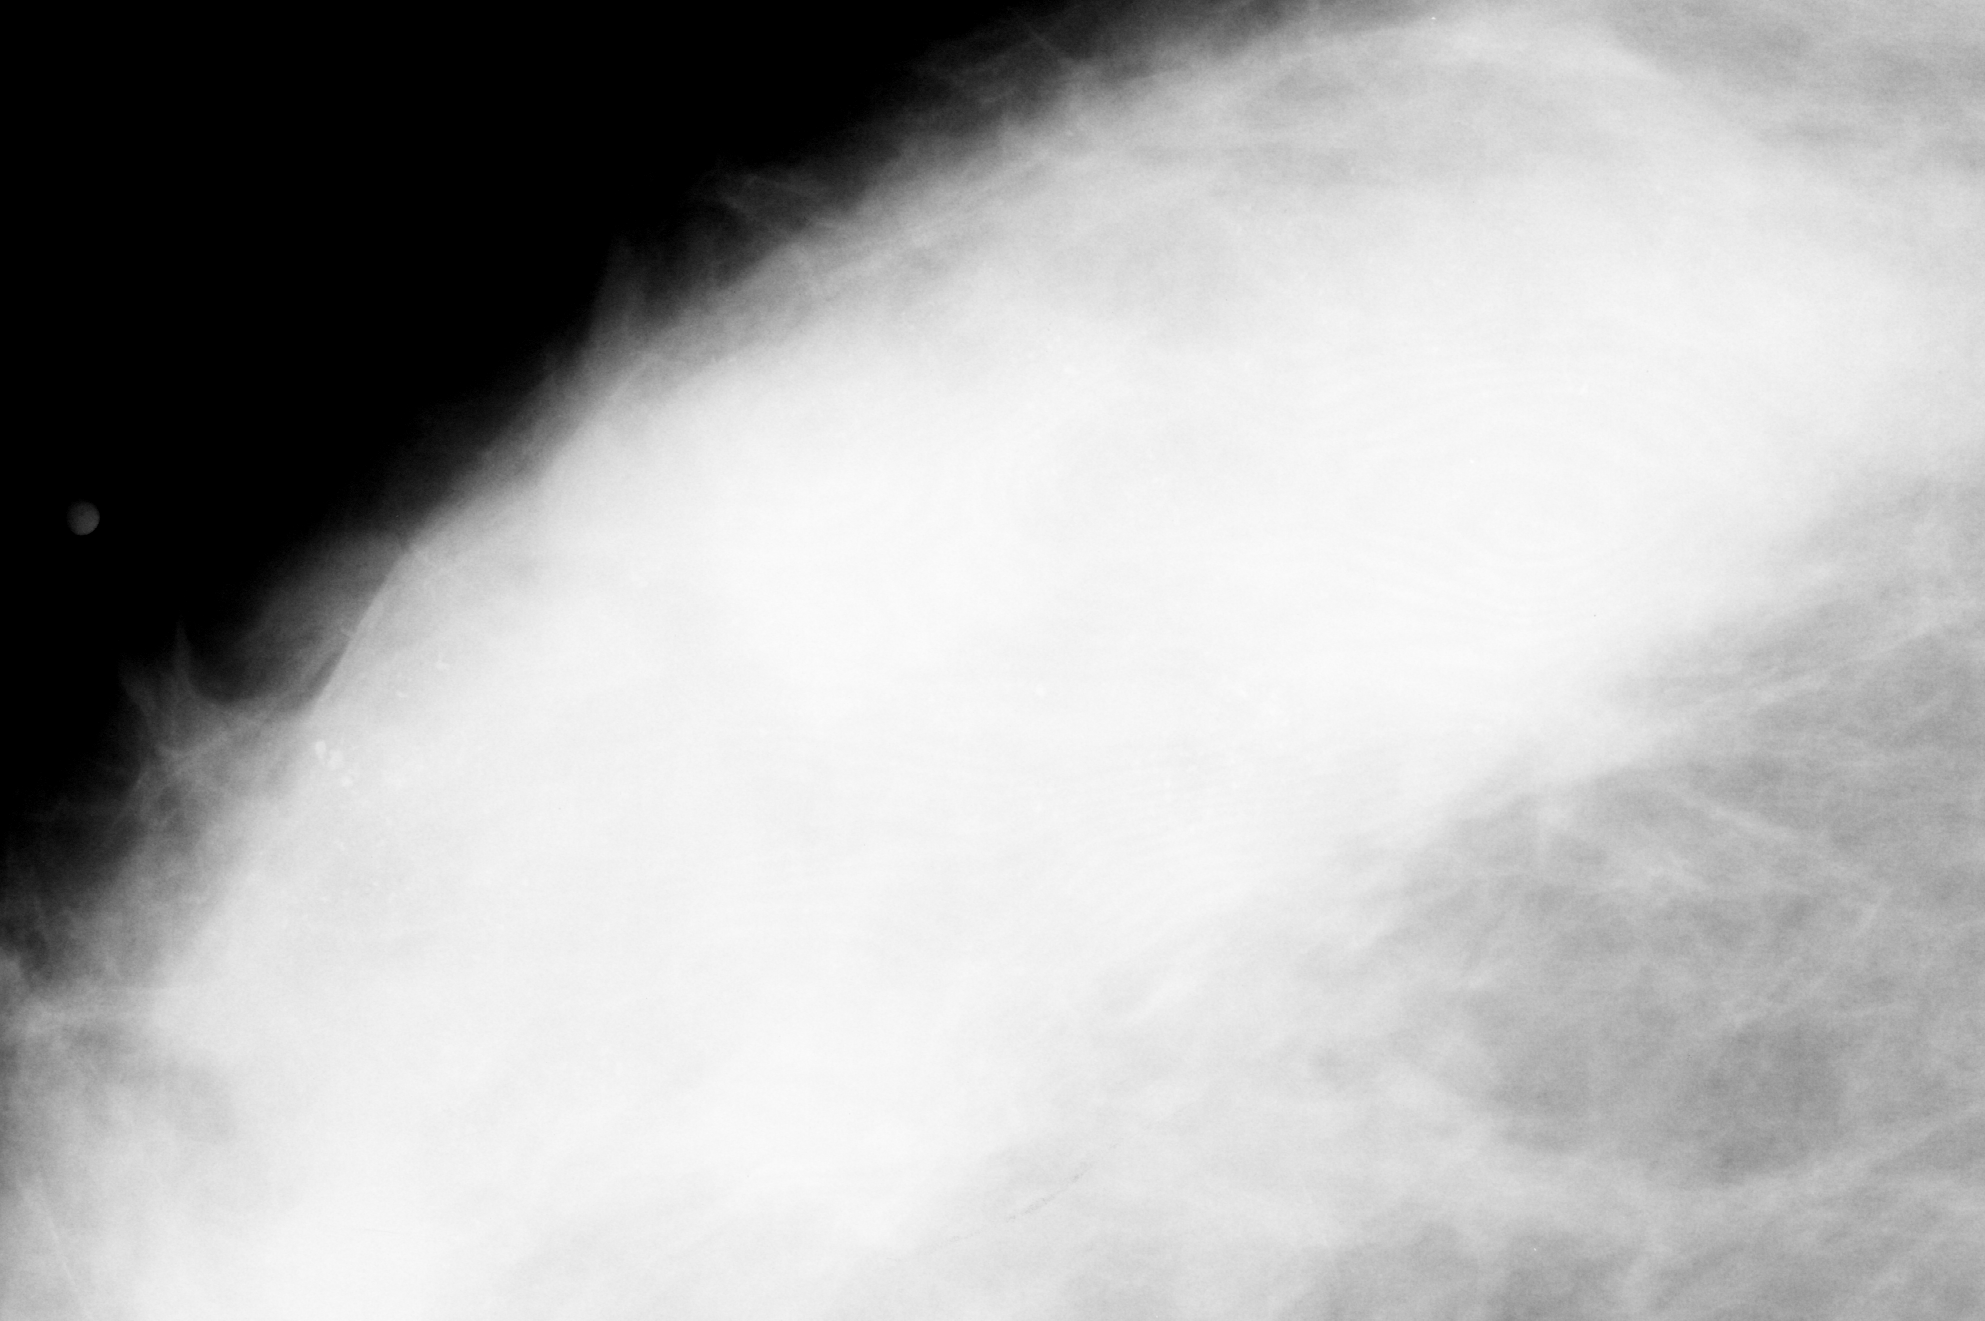
Crop from a digitized film mammogram around one marked abnormality, right breast, CC view.
Finding: calcifications, morphology pleomorphic, distribution regional; BI-RADS assessment category 4; subtlety rating 3 on a 1 (subtle) to 5 (obvious) scale; pathology (as recorded): malignant.